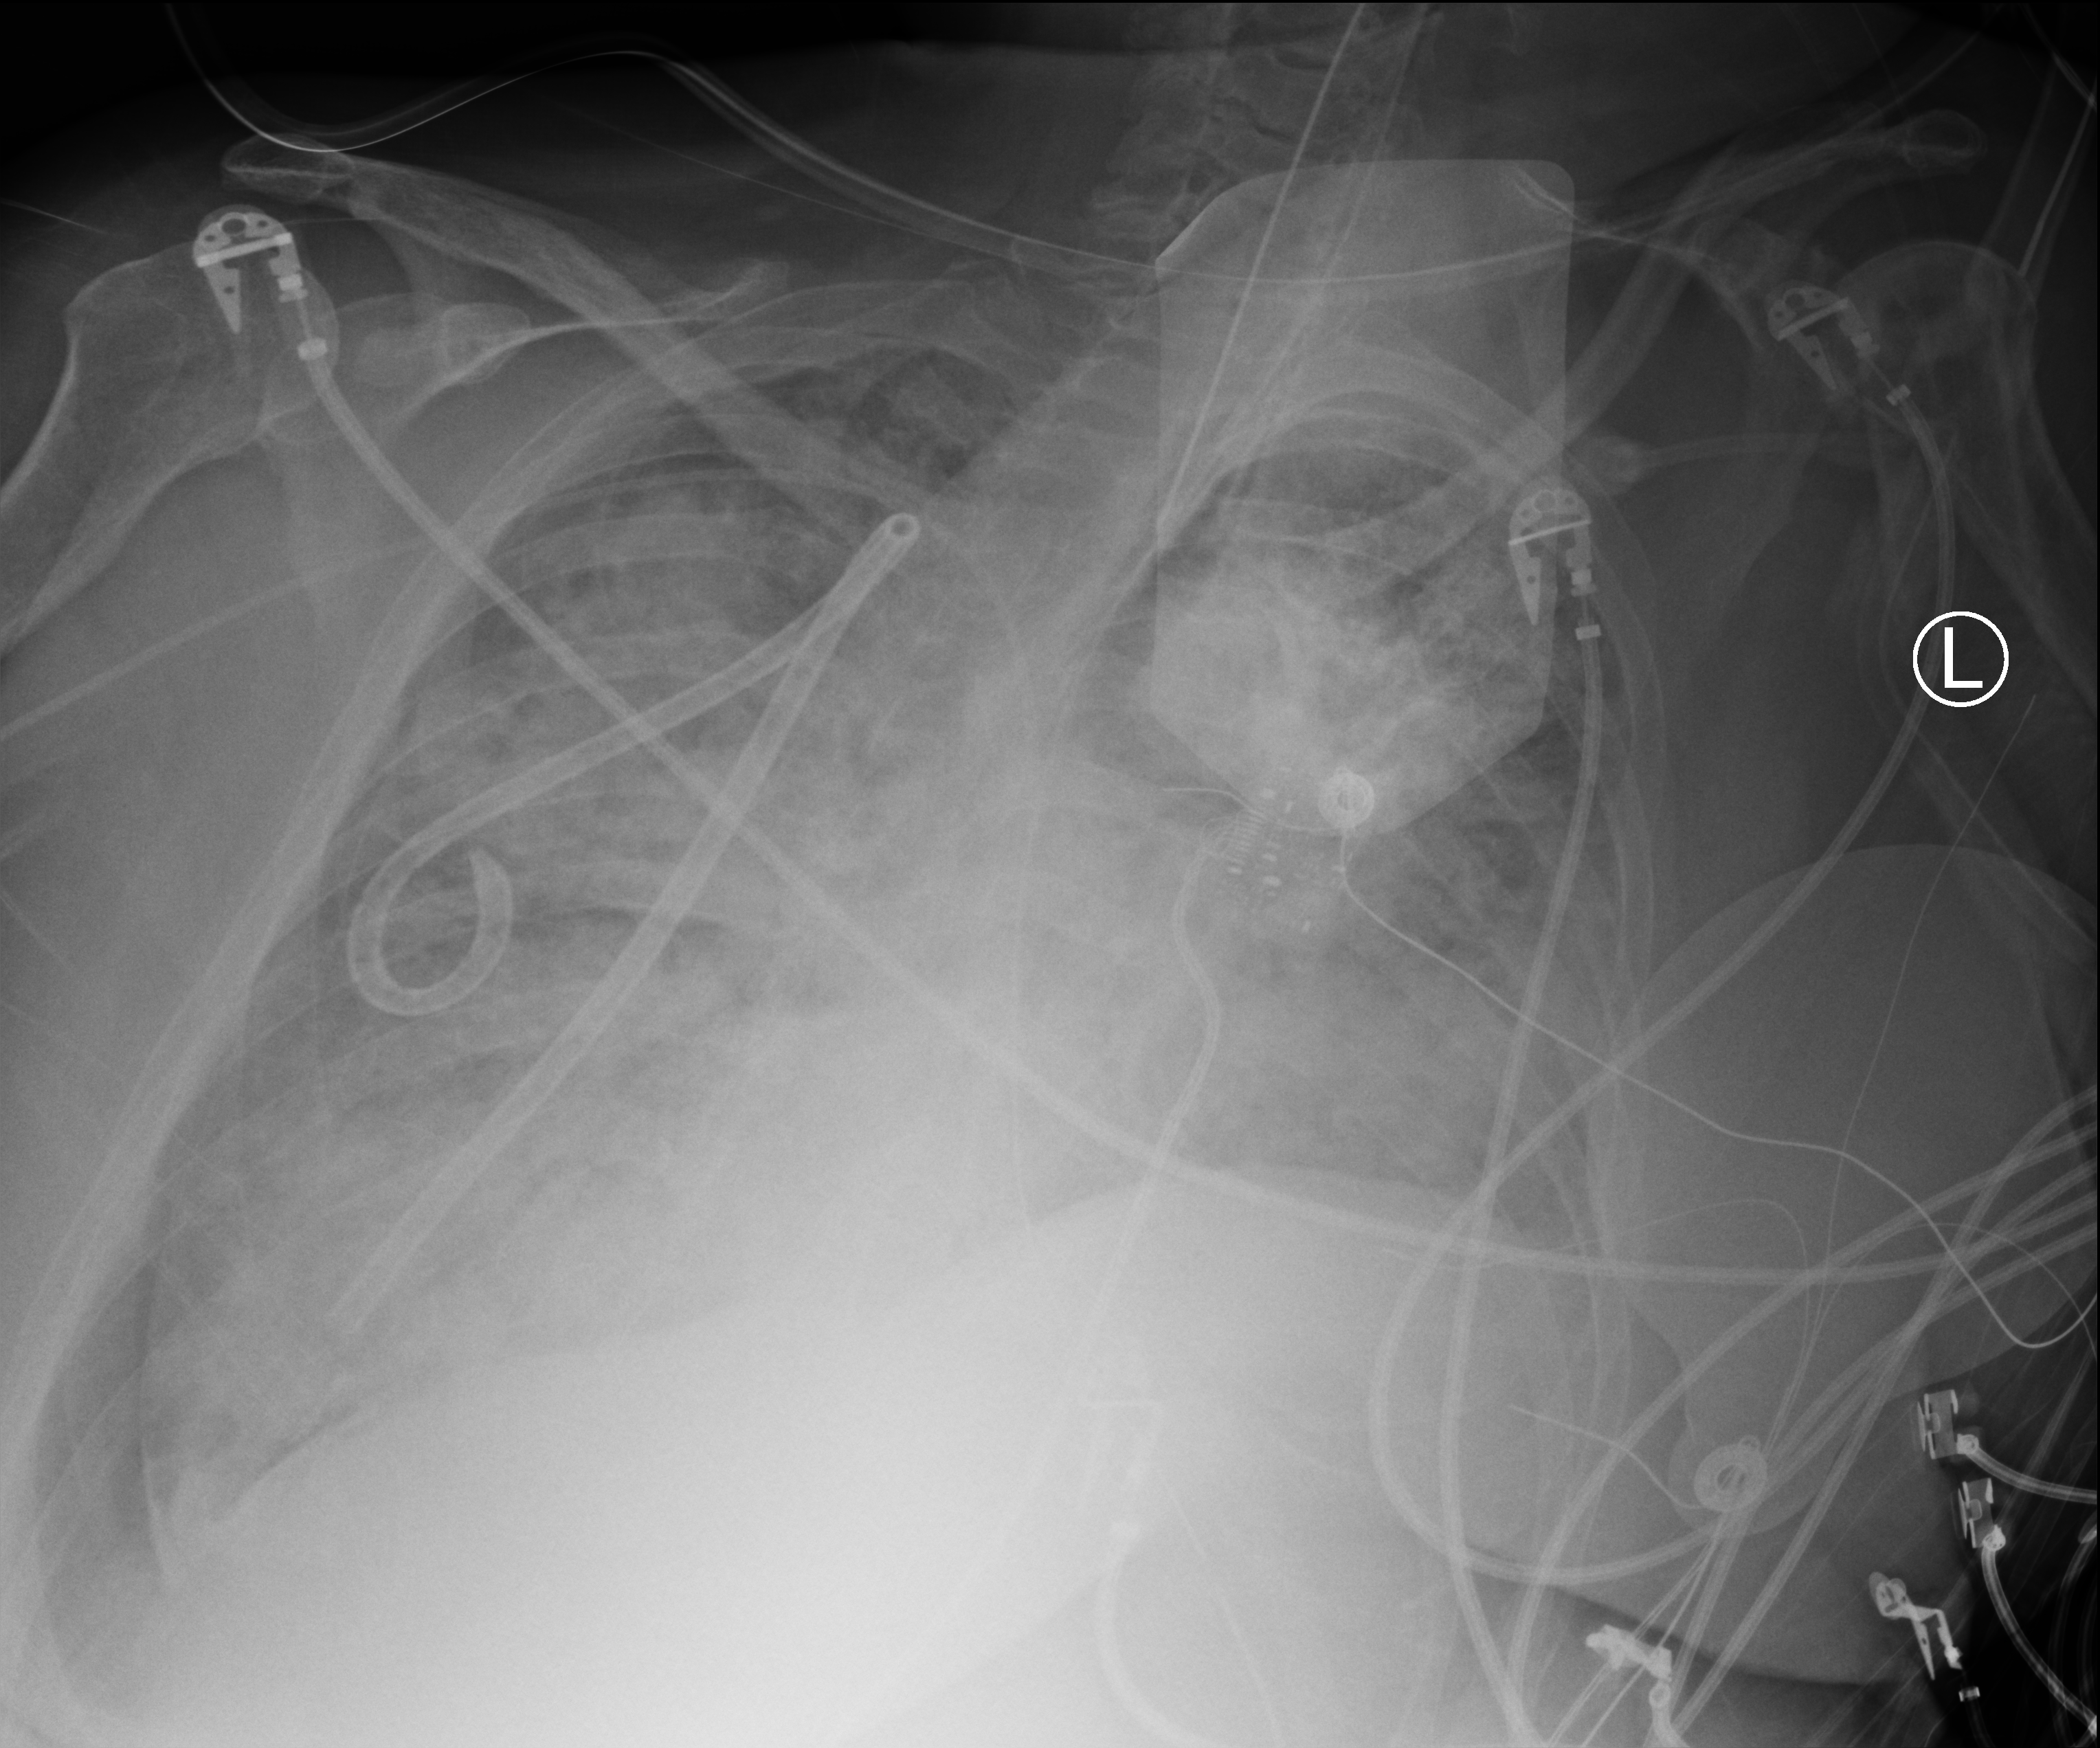
Bedside chest radiograph (computed radiography). Patient hospitalised with COVID-19, aged 18–59 years.
Hospital-stay facts (about this admission, not read from this image; timing relative to this image not recorded):
- mechanically ventilated during this hospital stay: yes